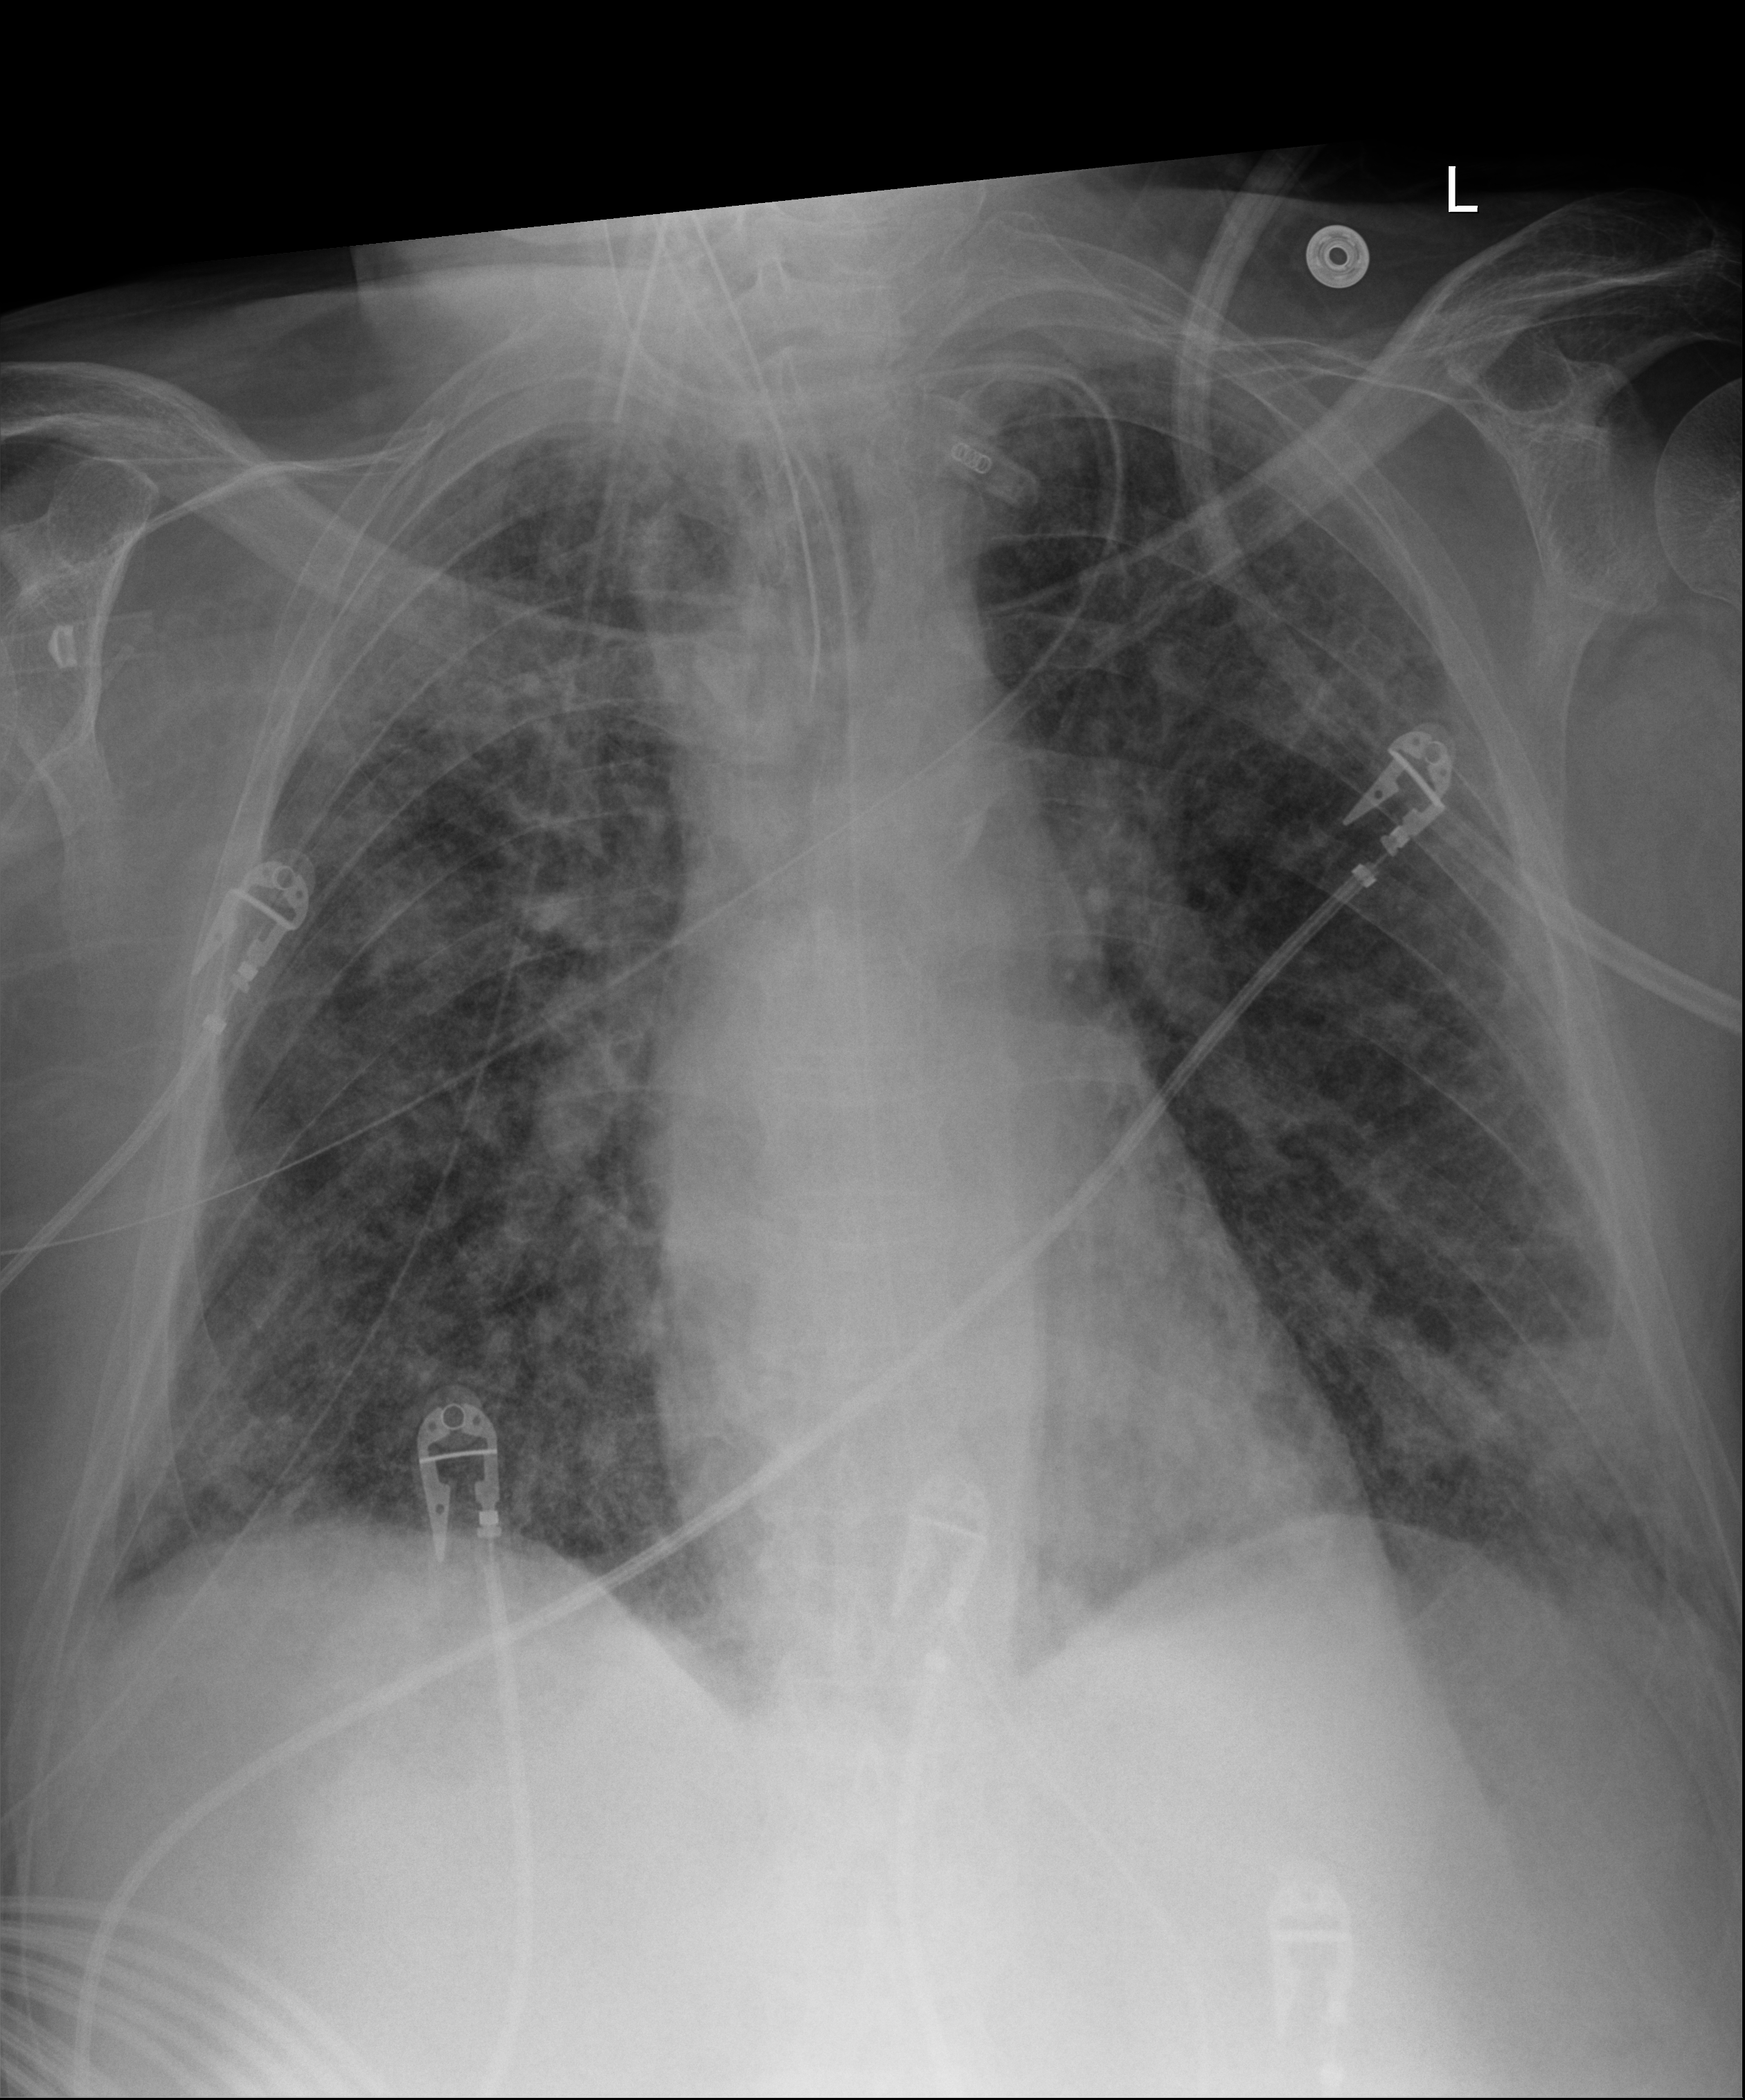
Bedside chest radiograph (digital radiography), anteroposterior (AP) projection. Male patient hospitalised with COVID-19, age 60–74 years.
From the hospital-stay record, not from the radiograph (when in the stay this image was taken is not recorded): mechanically ventilated during this hospital stay: yes.